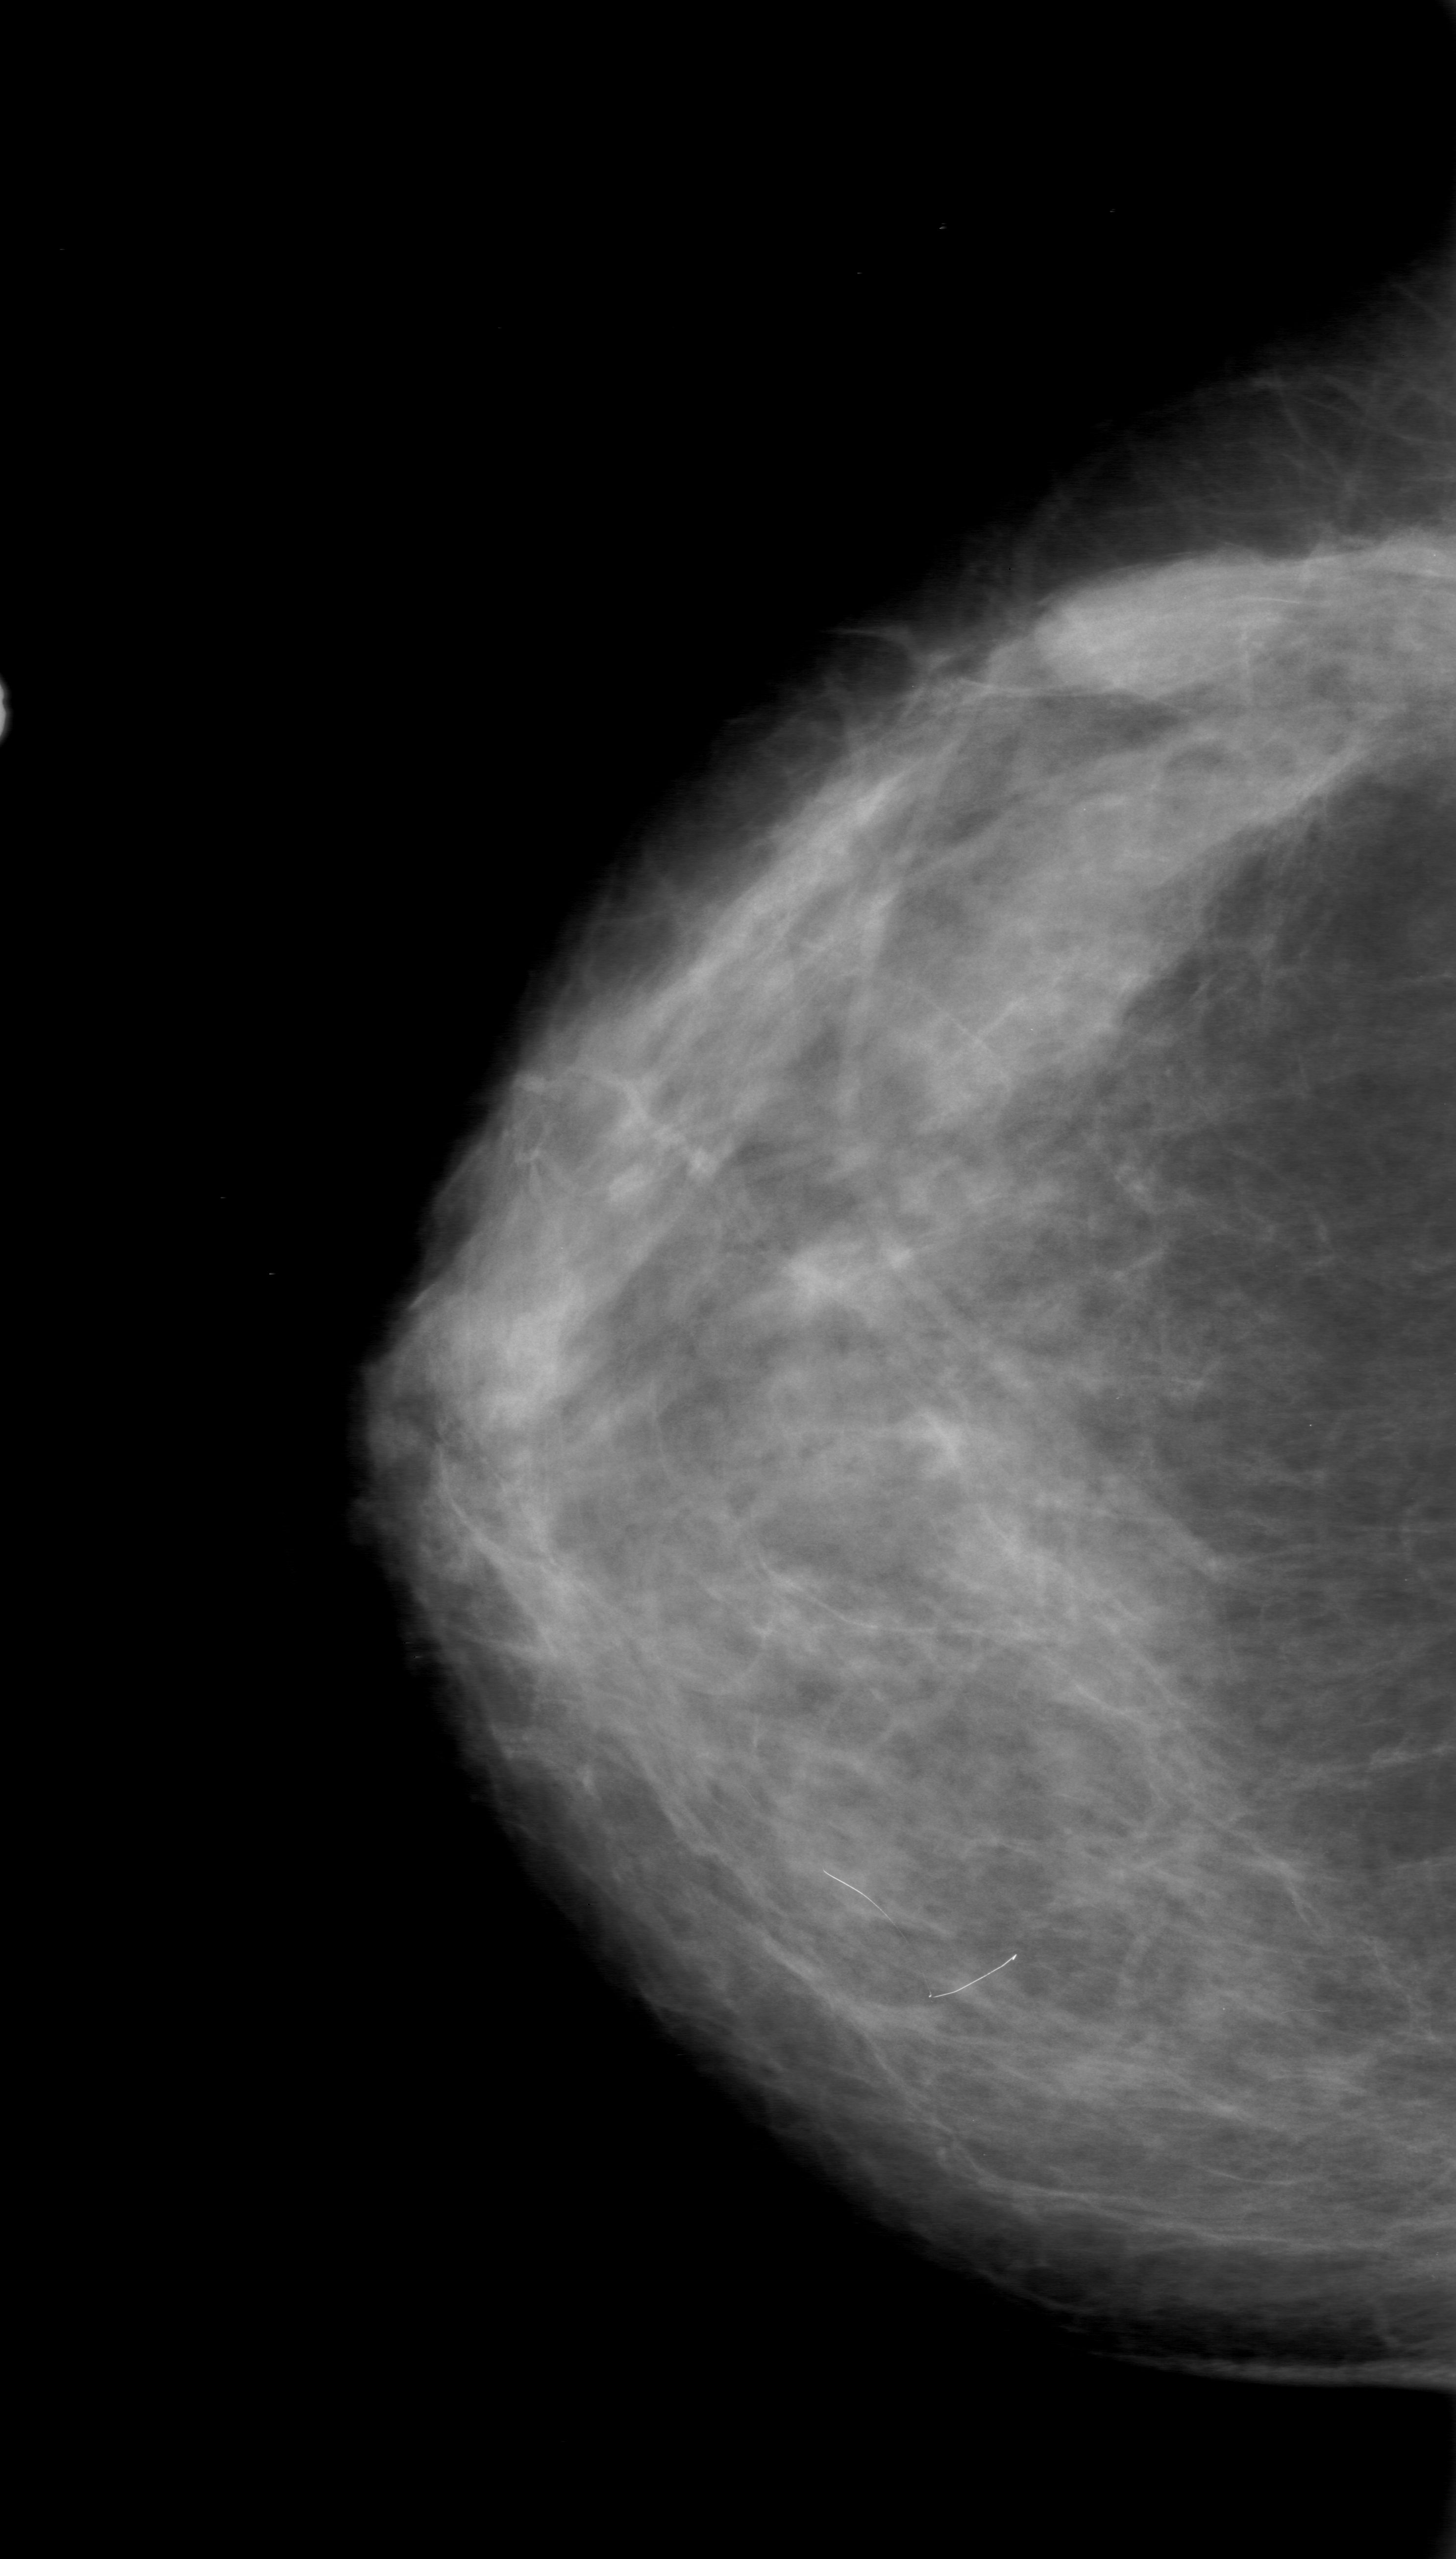
Scanned film-screen mammogram, right breast, craniocaudal (CC) view.
- Marked abnormality: mass, shape oval, margins obscured; BI-RADS assessment category 0; pathology result (as recorded, not read from the image): benign.